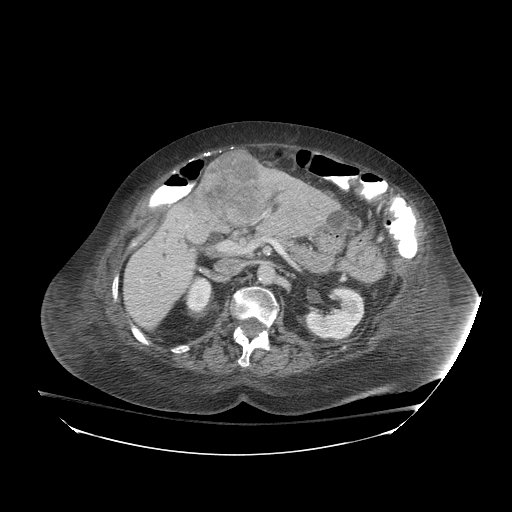
Contrast-enhanced abdominal CT (liver protocol), one axial slice; slice 38 of 81 in the series (ordered by position); reconstruction kernel STANDARD; soft-tissue window (W 400 / L 40 HU); 2.5 mm slice thickness; 512 × 512 image matrix. Case-level facts recorded for this patient, not image findings: diagnosis: hepatocellular carcinoma (patient treated with transarterial chemoembolisation; whether this scan precedes or follows treatment is not stated here); TNM stage (as recorded): Stage-I; Child-Pugh class: B; tumour nodularity: uninodular.
Outlined on this slice (semi-automatically segmented with operator editing):
- liver parenchyma outside the tumour (the mass and vessels are separate outlines, so this box may not span the whole liver): bounding box <122,172,338,328> (left, top, right, bottom; pixels)
- mass: <200,150,267,225>
- liver vessels: <186,225,188,227>